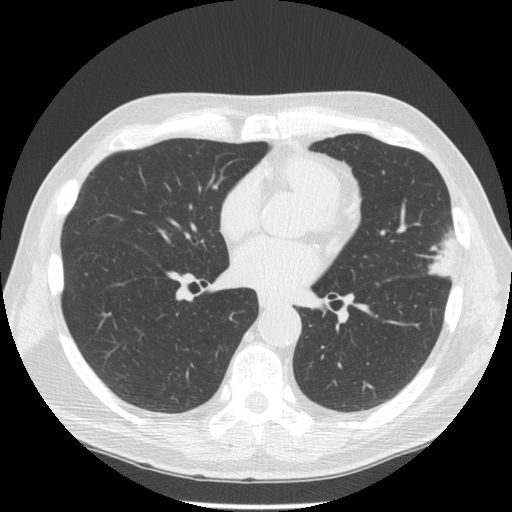
Low-dose screening chest CT, one axial slice. Position 67 of 134 along the scan axis. Reconstruction kernel STANDARD. Lung window (W 1500 / L -600 HU). 2.5 mm slice thickness. 512 × 512 image matrix.
Outlined on this slice (outlined manually by an expert reader):
- lesion 1 (tumor, upper lobe of left lung): bounding box (x1, y1, x2, y2) in pixels: (429, 230, 457, 277)